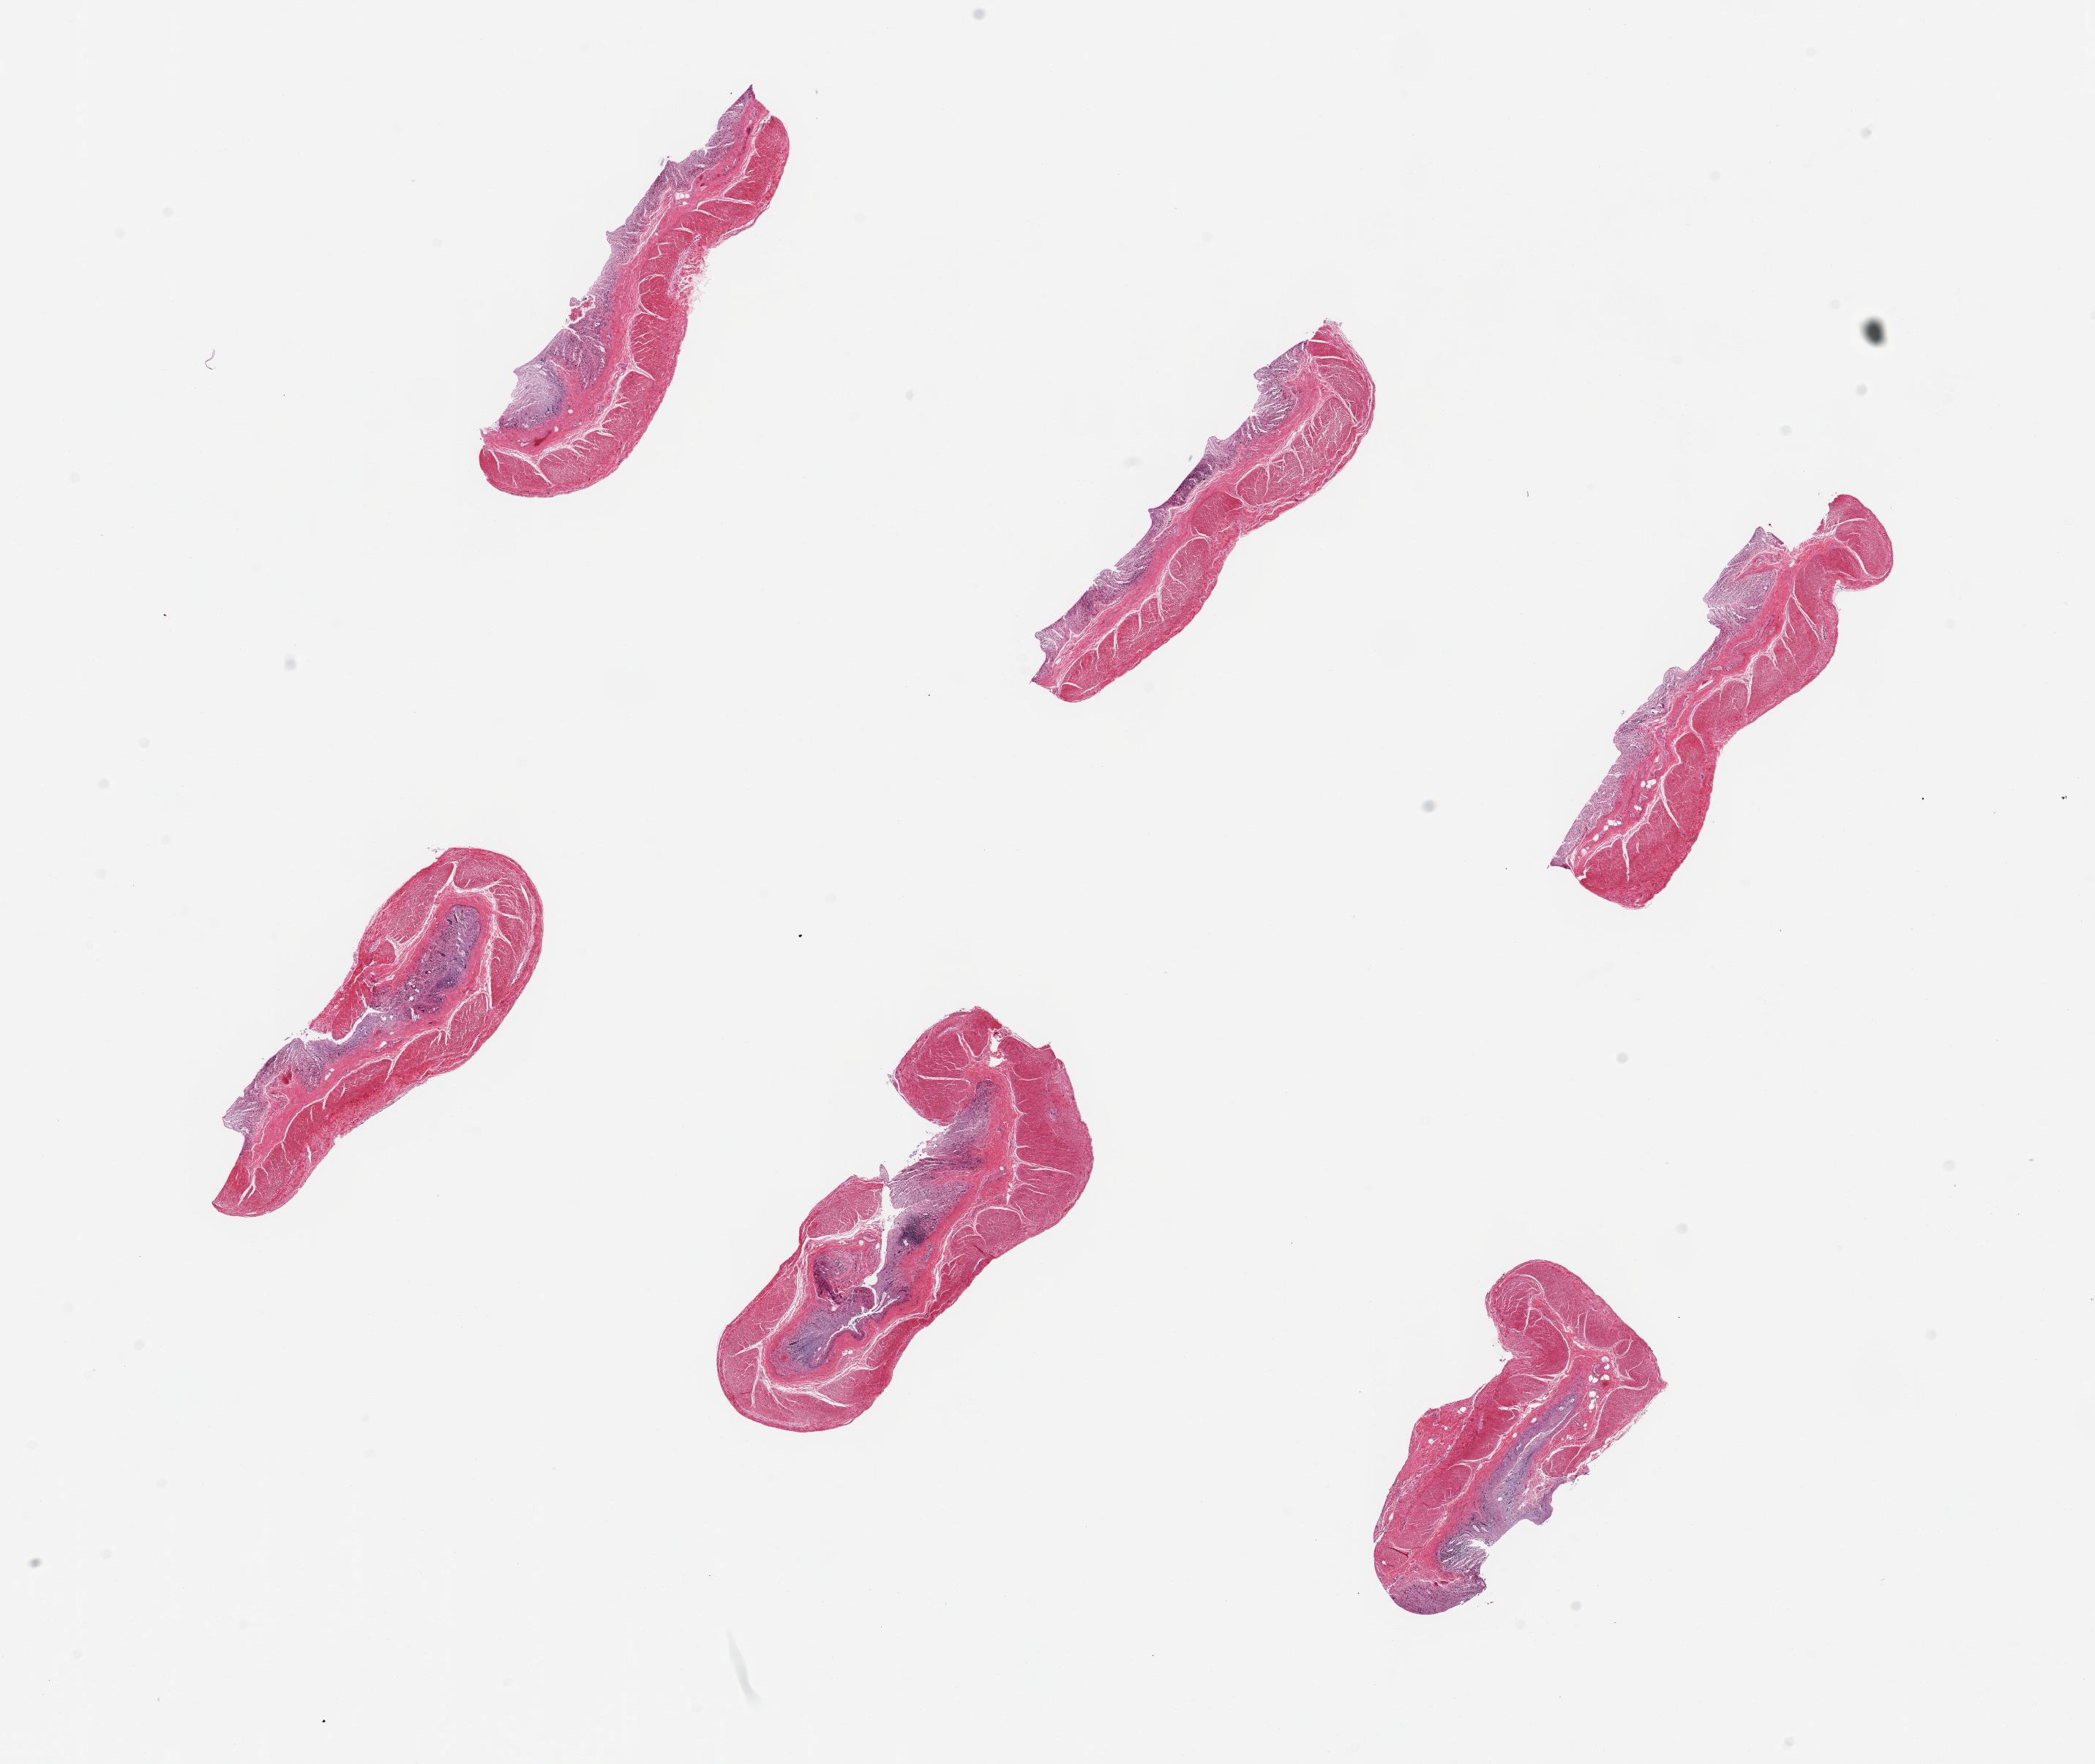
Whole-slide image, haematoxylin and eosin stain — low-resolution overview of the scanned area, about 22.6 x 19.1 mm. PAXgene-fixed paraffin-embedded (PFPE) section. Section of transverse colon (target tissue). Donor tissue sample. Donor: female.
* pathologist's review note for this sample: 6 pieces. up to 5x2mm; mucosa=3; muscularis=2